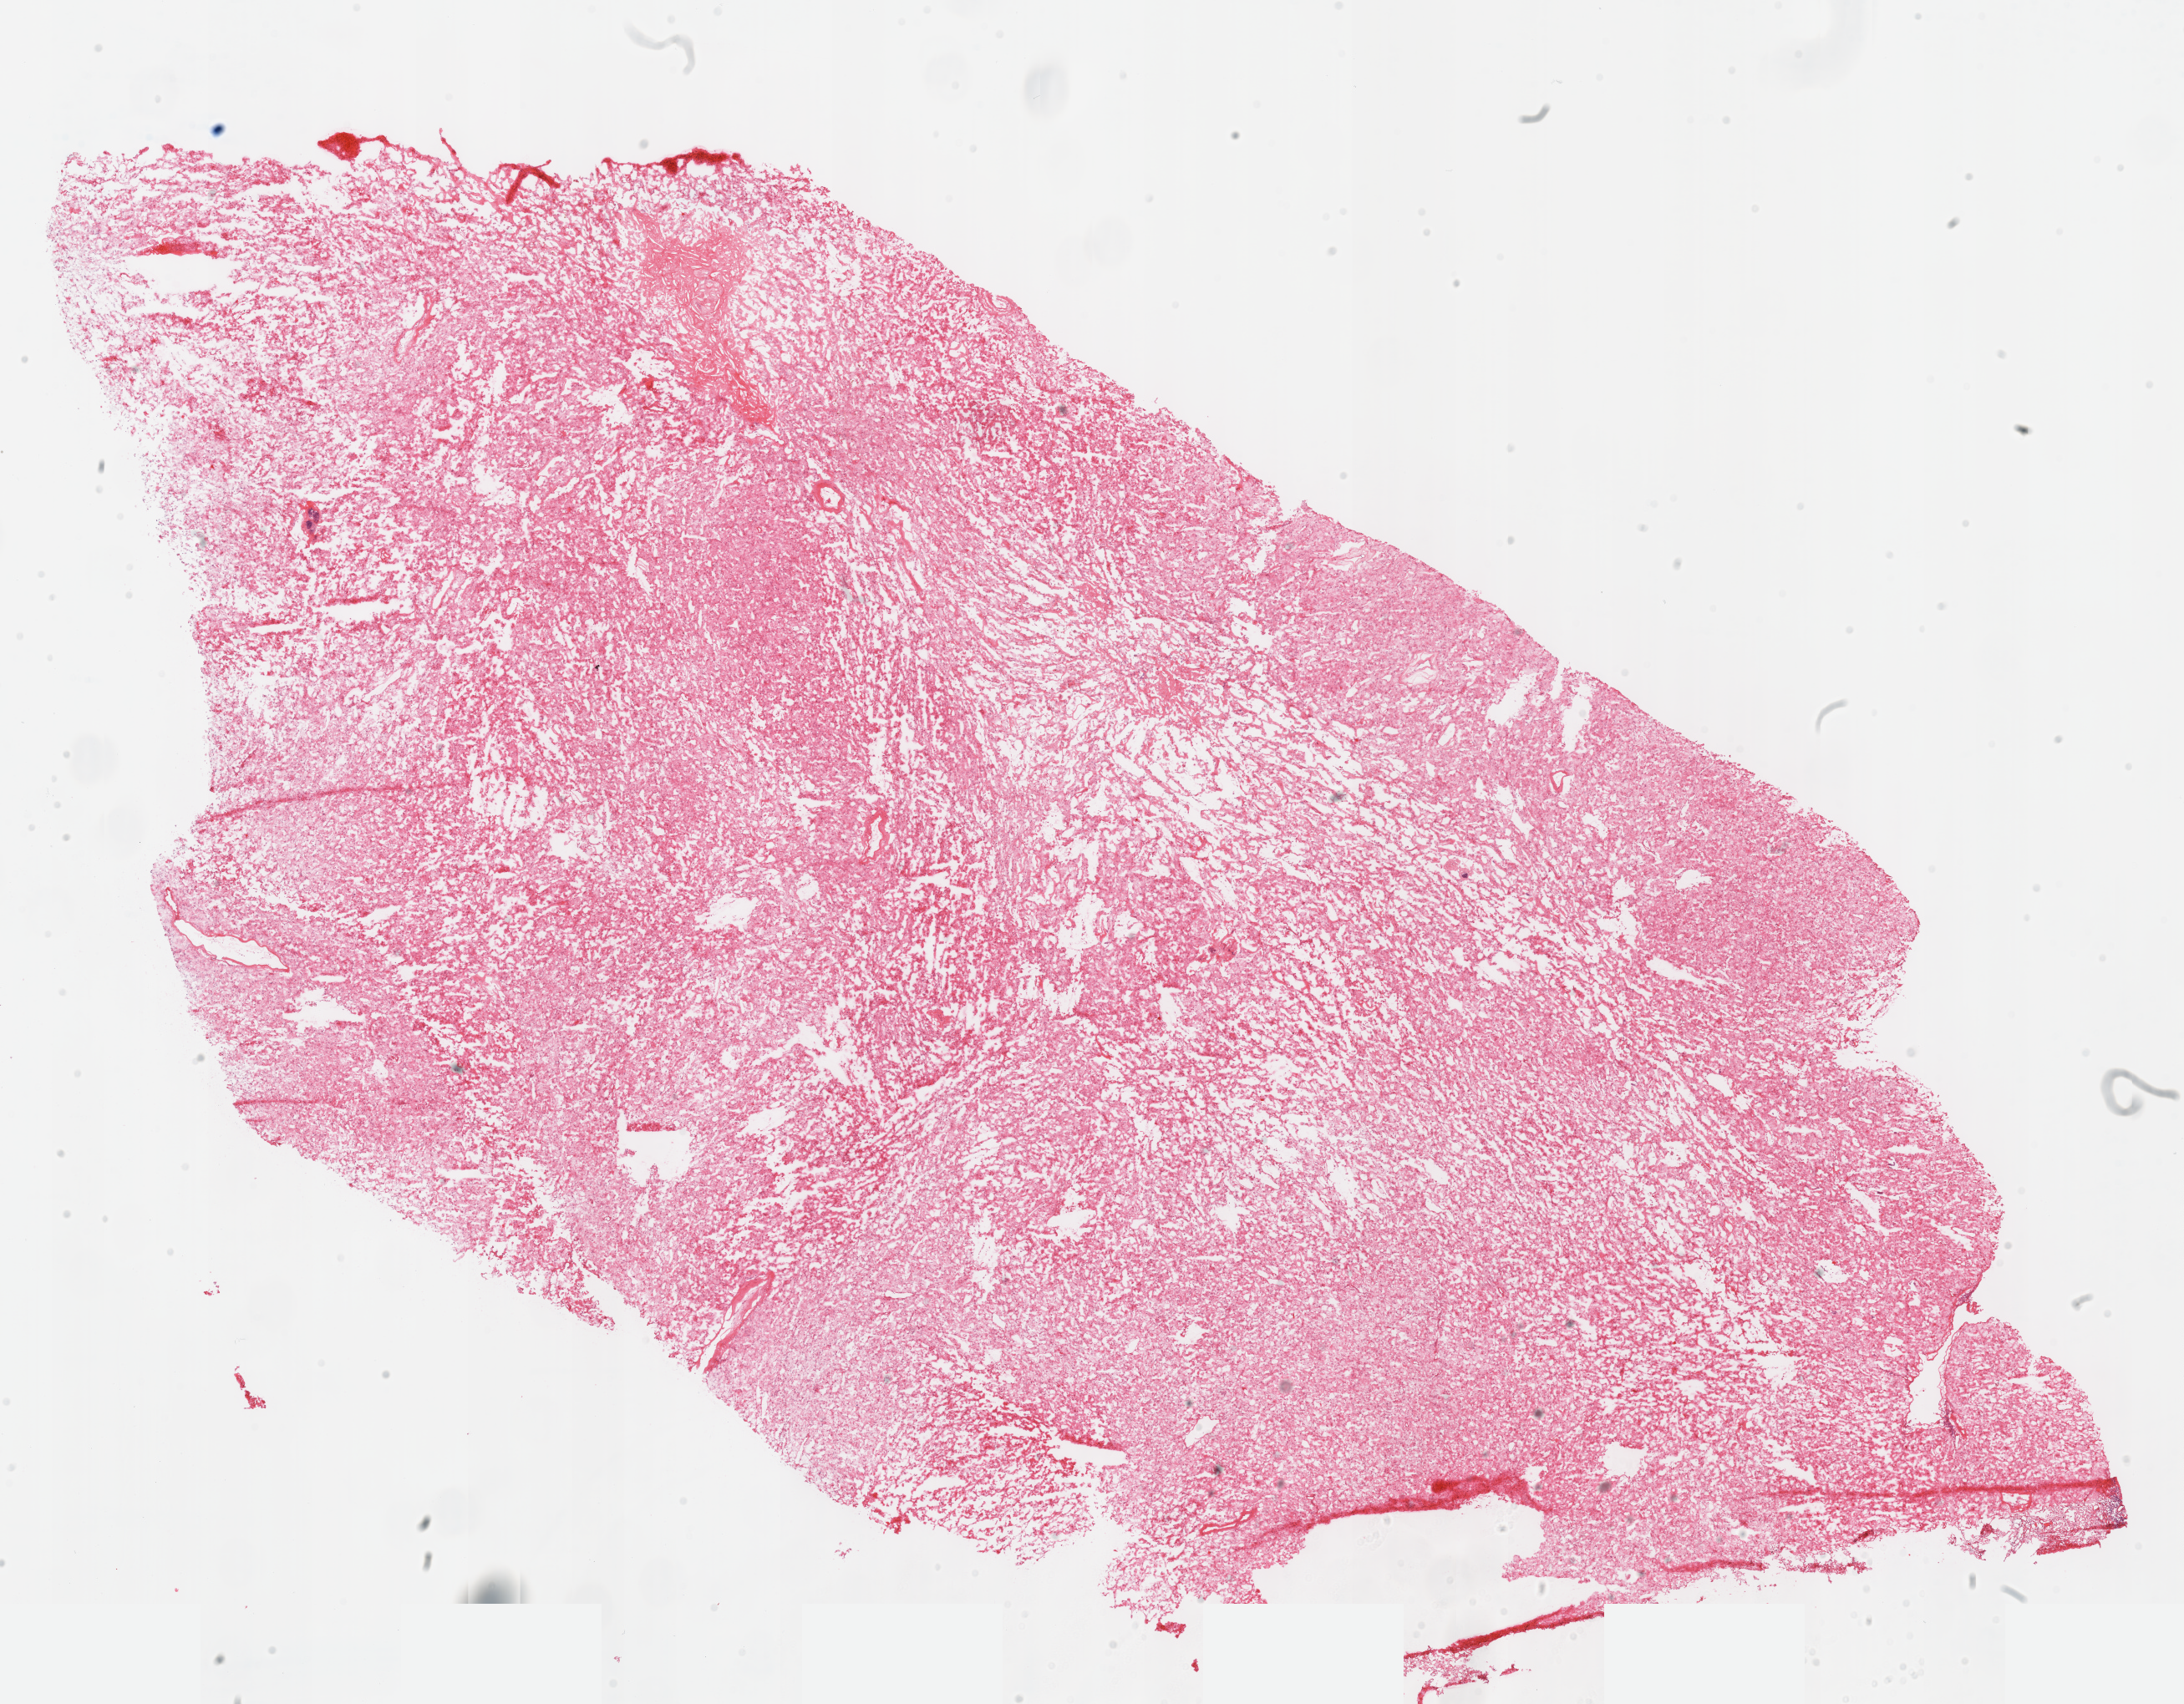
Digitized H&E-stained tissue section (whole slide) — a low-resolution overview of the entire scanned area, about 20.6 x 16.0 mm. Frozen section from the top of the tissue portion. Kidney, primary tumour sample. Male patient; age at initial diagnosis 53 years. Pathologist review of this section (percent, as recorded): tumour cells 100%, tumour nuclei 80%, normal cells 0%, stromal cells 0%, necrosis 0%. Inflammatory infiltration, as recorded: lymphocyte infiltration 0%, monocyte infiltration 10%, neutrophil infiltration 0%.
AJCC pathologic stage: I (6th edition). Diagnosis: Renal cell carcinoma, chromophobe type. TNM: T1b N0.